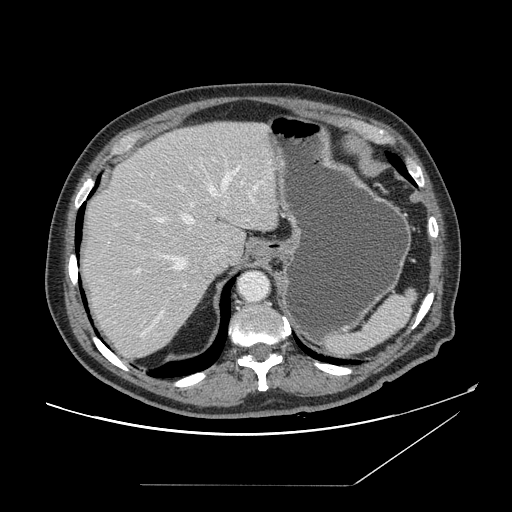
Contrast-enhanced abdominal CT, one axial slice; slice 119 of 166 in the series (ordered by position); 120 kVp; intravenous contrast given; soft-tissue window (W 400 / L 40 HU); 2.5 mm slice thickness; 512 × 512 image matrix, field of view 416 × 416 mm. Male patient, age 80 years. Case-level facts recorded for this patient, not image findings: diagnosis: colorectal cancer liver metastases, imaged before liver resection; multiple liver metastases: no; largest metastasis: 2.2 cm; chemotherapy before resection: no.
Annotated regions visible in this slice (manually delineated by an expert):
- hepatic veins: bounding box [x1, y1, x2, y2] px = [154, 167, 240, 271]
- liver: [80, 122, 279, 358]
- planned liver remnant (the part of the liver to remain after resection): [83, 121, 279, 263]
- portal vein (with intrahepatic branches): [135, 182, 263, 274]